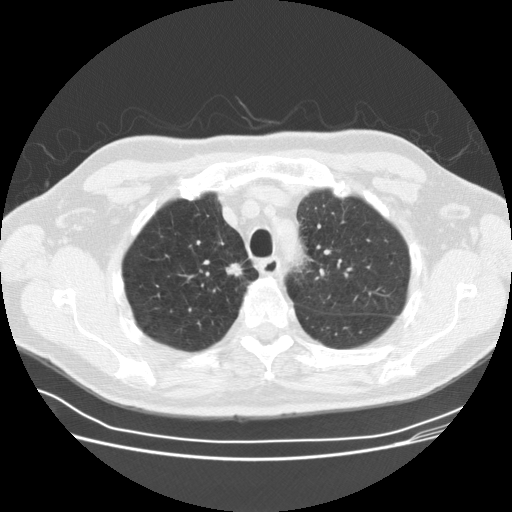
Low-dose screening chest CT, one axial slice. Reconstruction kernel STANDARD. Lung window (W 1500 / L -600 HU). 2.5 mm slice thickness. 512 × 512 image matrix, field of view 360 × 360 mm.
Annotated regions visible in this slice (outlined manually by an expert reader):
- lesion 1 (tumor, upper lobe of right lung): box from (x=226, y=263) to (x=243, y=277) px